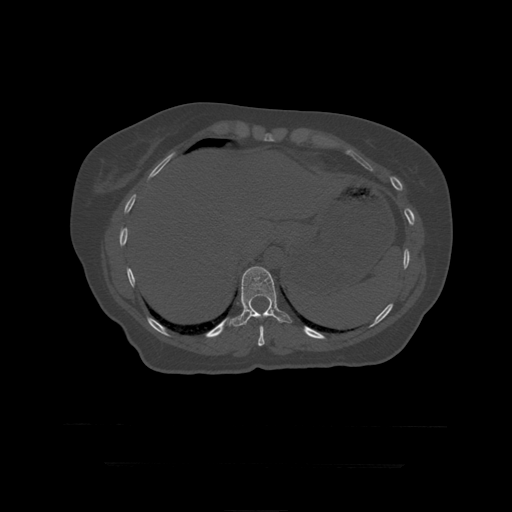
CT including the spine, one axial slice. Slice 225 of 399 in the series (ordered by position). Bone window (W 1800 / L 400 HU). 1.25 mm slice thickness. 512 × 512 image matrix, field of view 450 × 450 mm. Patient age 41 years. From the clinical record (not read from this slice): primary cancer: breast.
Annotated regions visible in this slice (semi-automatic segmentation, software-assisted and operator-edited):
- T10 vertebra: bounding box [x1, y1, x2, y2] px = [258, 326, 265, 347]
- T11 vertebra: [224, 267, 292, 327]